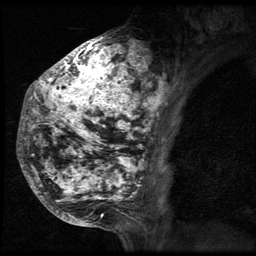
Breast MRI (dynamic contrast-enhanced), one sagittal slice; slice 25 of 64 in the series (ordered by position); 3 images stored at this slice position (order not interpretable as contrast timing); 1.5 T; TE 4.2 ms, TR 9 ms; 2.5 mm slice thickness; 256 × 256 image matrix, field of view 180 × 180 mm. Patient: female, 50 years. Case-level facts recorded for this patient, not image findings: setting: breast cancer imaged before/during neoadjuvant chemotherapy; receptor status: triple-negative.
Outlined on this slice (semi-automatically segmented with operator editing):
- analysis volume of interest (the breast-tissue region the enhancement analysis was run in; not a lesion): bounding box <24,39,164,212> (left, top, right, bottom; pixels)
- tumour enhancement mask (voxels above the 140 % enhancement threshold inside the analysis volume of interest): <24,39,164,209>